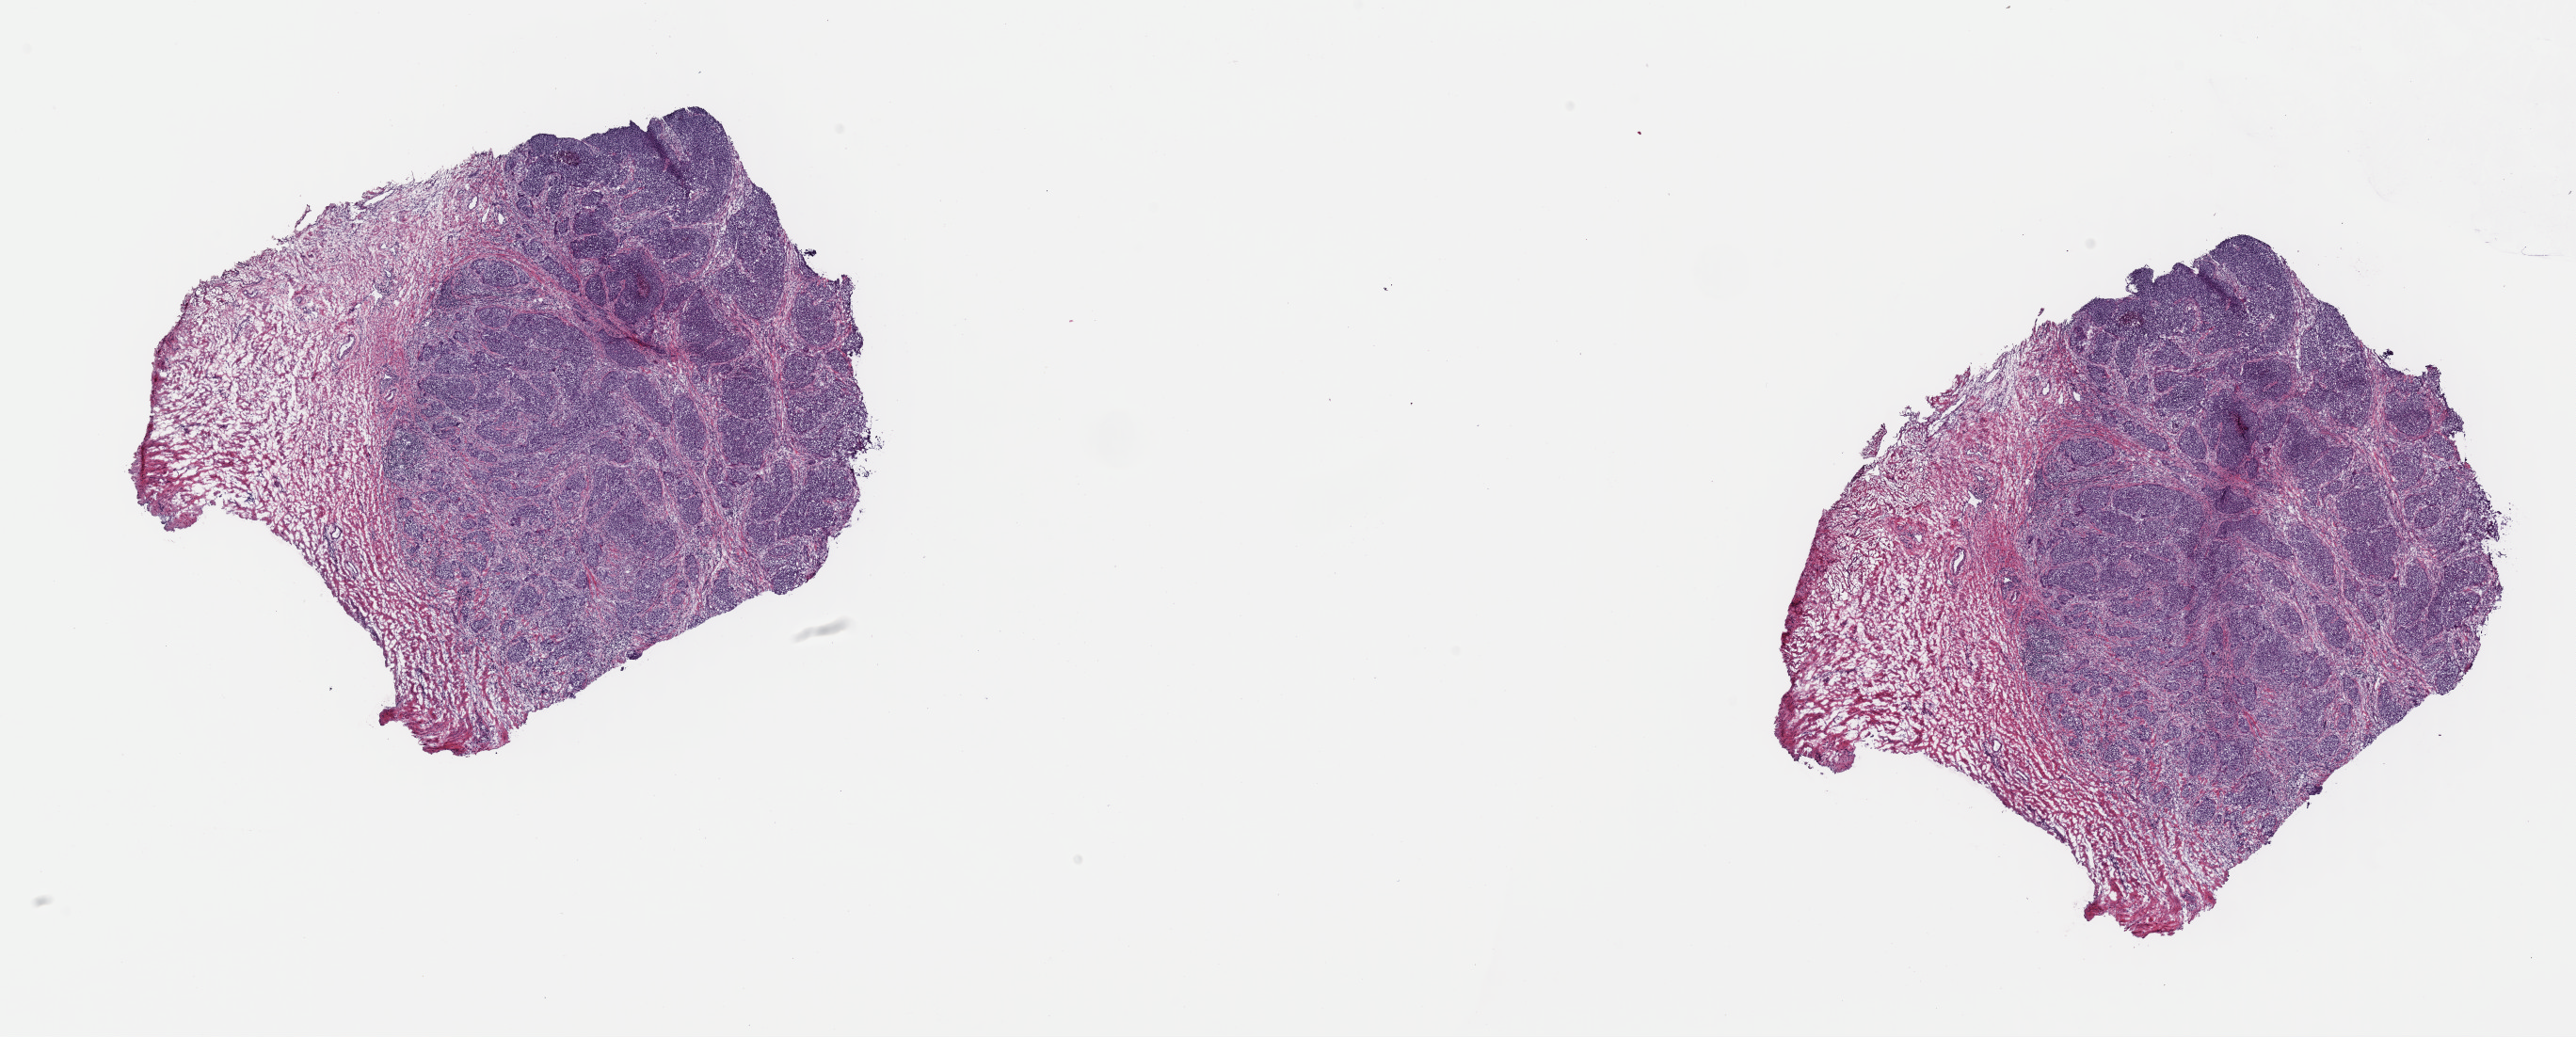
Digitized H&E-stained tissue section (whole slide) — whole scanned area (about 21.6 x 8.7 mm) shown as a low-resolution overview. Frozen section. Primary tumour sample from the cervix. Patient: female, age at initial diagnosis 60 years. Histologic grade: G2 (moderately differentiated). Pathologist review of this section (percent, as recorded): tumour cells 75%, tumour nuclei 80%, normal cells 25%, stromal cells 0%, necrosis 0%. Inflammatory infiltration, as recorded: lymphocyte infiltration 4%, monocyte infiltration 0%, neutrophil infiltration 0%.
Lymph nodes positive (case pathology): 0 of 13 examined. Pathologic diagnosis: Squamous cell carcinoma, NOS. FIGO stage: II.